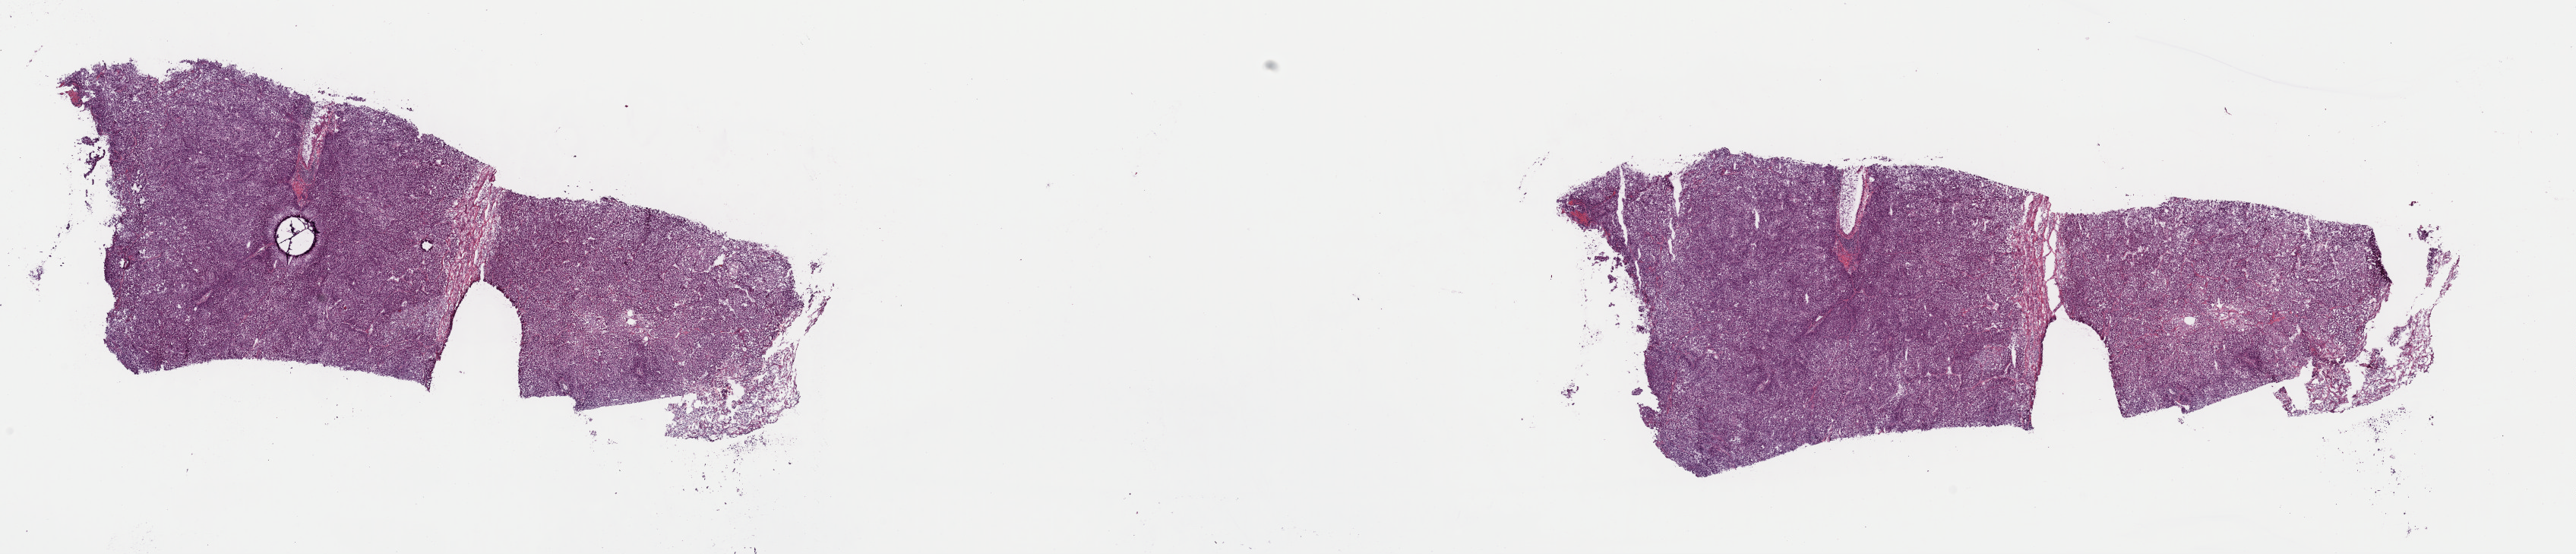
Digitized H&E-stained tissue section (whole slide), whole scanned area (about 26.8 x 5.8 mm, acquisition: 40x scan) shown as a low-resolution overview; frozen section from the top of the tissue portion; liver, primary tumour sample. Patient: male, age at initial diagnosis 77 years. Histologic grade: G2 (moderately differentiated). Composition of this section per pathologist review: tumour cells 90%, tumour nuclei 100%, normal cells 0%, stromal cells 10%, necrosis 0%. Infiltration values recorded for this section: lymphocyte infiltration 6%, monocyte infiltration 1%, neutrophil infiltration 1%.
AJCC pathologic stage: IIIA (7th edition). Pathologic diagnosis: Hepatocellular carcinoma, NOS. TNM: T3a NX M0.